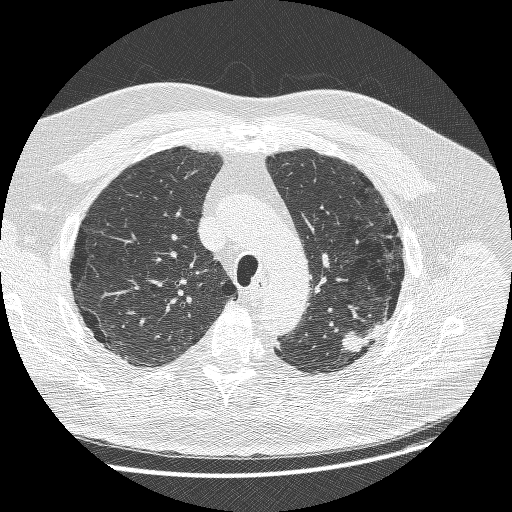
Axial slice from a low-dose chest CT screening exam; baseline screening round; lung window (W 1500 / L -600 HU); 1.25 mm slice thickness; slice 198 of 258 in the series. Male participant, aged 68 years at enrolment. Former smoker at enrolment.
Expert reader's lesion annotation, bounding box [x1, y1, x2, y2] px = [334, 312, 390, 362]. Screening reader's record for this exam (one nodule recorded; not confirmed to be the boxed lesion): non-calcified nodule or mass ≥4 mm, left upper lobe, 15 × 14 mm, smooth margins, soft tissue attenuation. Lung cancer was diagnosed 19 days after this screen: adenosquamous carcinoma, left upper lobe, poorly differentiated (G3), stage IIIB (AJCC 6th edition), 32 mm at pathology.